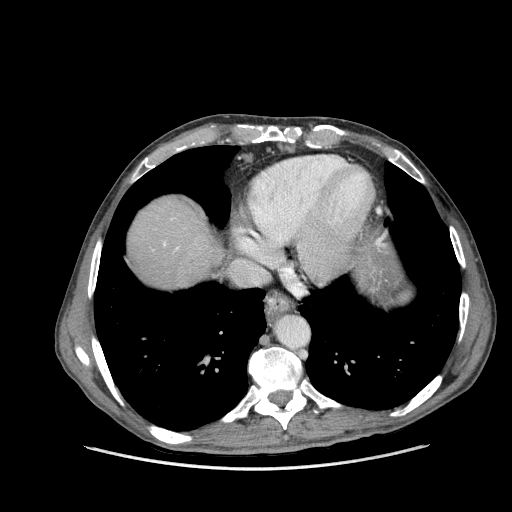
Contrast-enhanced abdominal CT (liver protocol), one axial slice. Reconstruction kernel STANDARD. 100 kVp. Soft-tissue window (W 400 / L 40 HU). 512 × 512 image matrix, field of view 400 × 400 mm. From the clinical record (not read from this slice): diagnosis: hepatocellular carcinoma (patient treated with transarterial chemoembolisation; whether this scan precedes or follows treatment is not stated here); TNM stage (as recorded): Stage-IIIA.
Outlined on this slice (semi-automatically segmented with operator editing):
- abdominal aorta: bounding box [x1, y1, x2, y2] px = [277, 316, 308, 348]
- liver parenchyma outside the tumour (the mass and vessels are separate outlines, so this box may not span the whole liver): [128, 198, 224, 288]
- liver vessels: [164, 243, 178, 249]